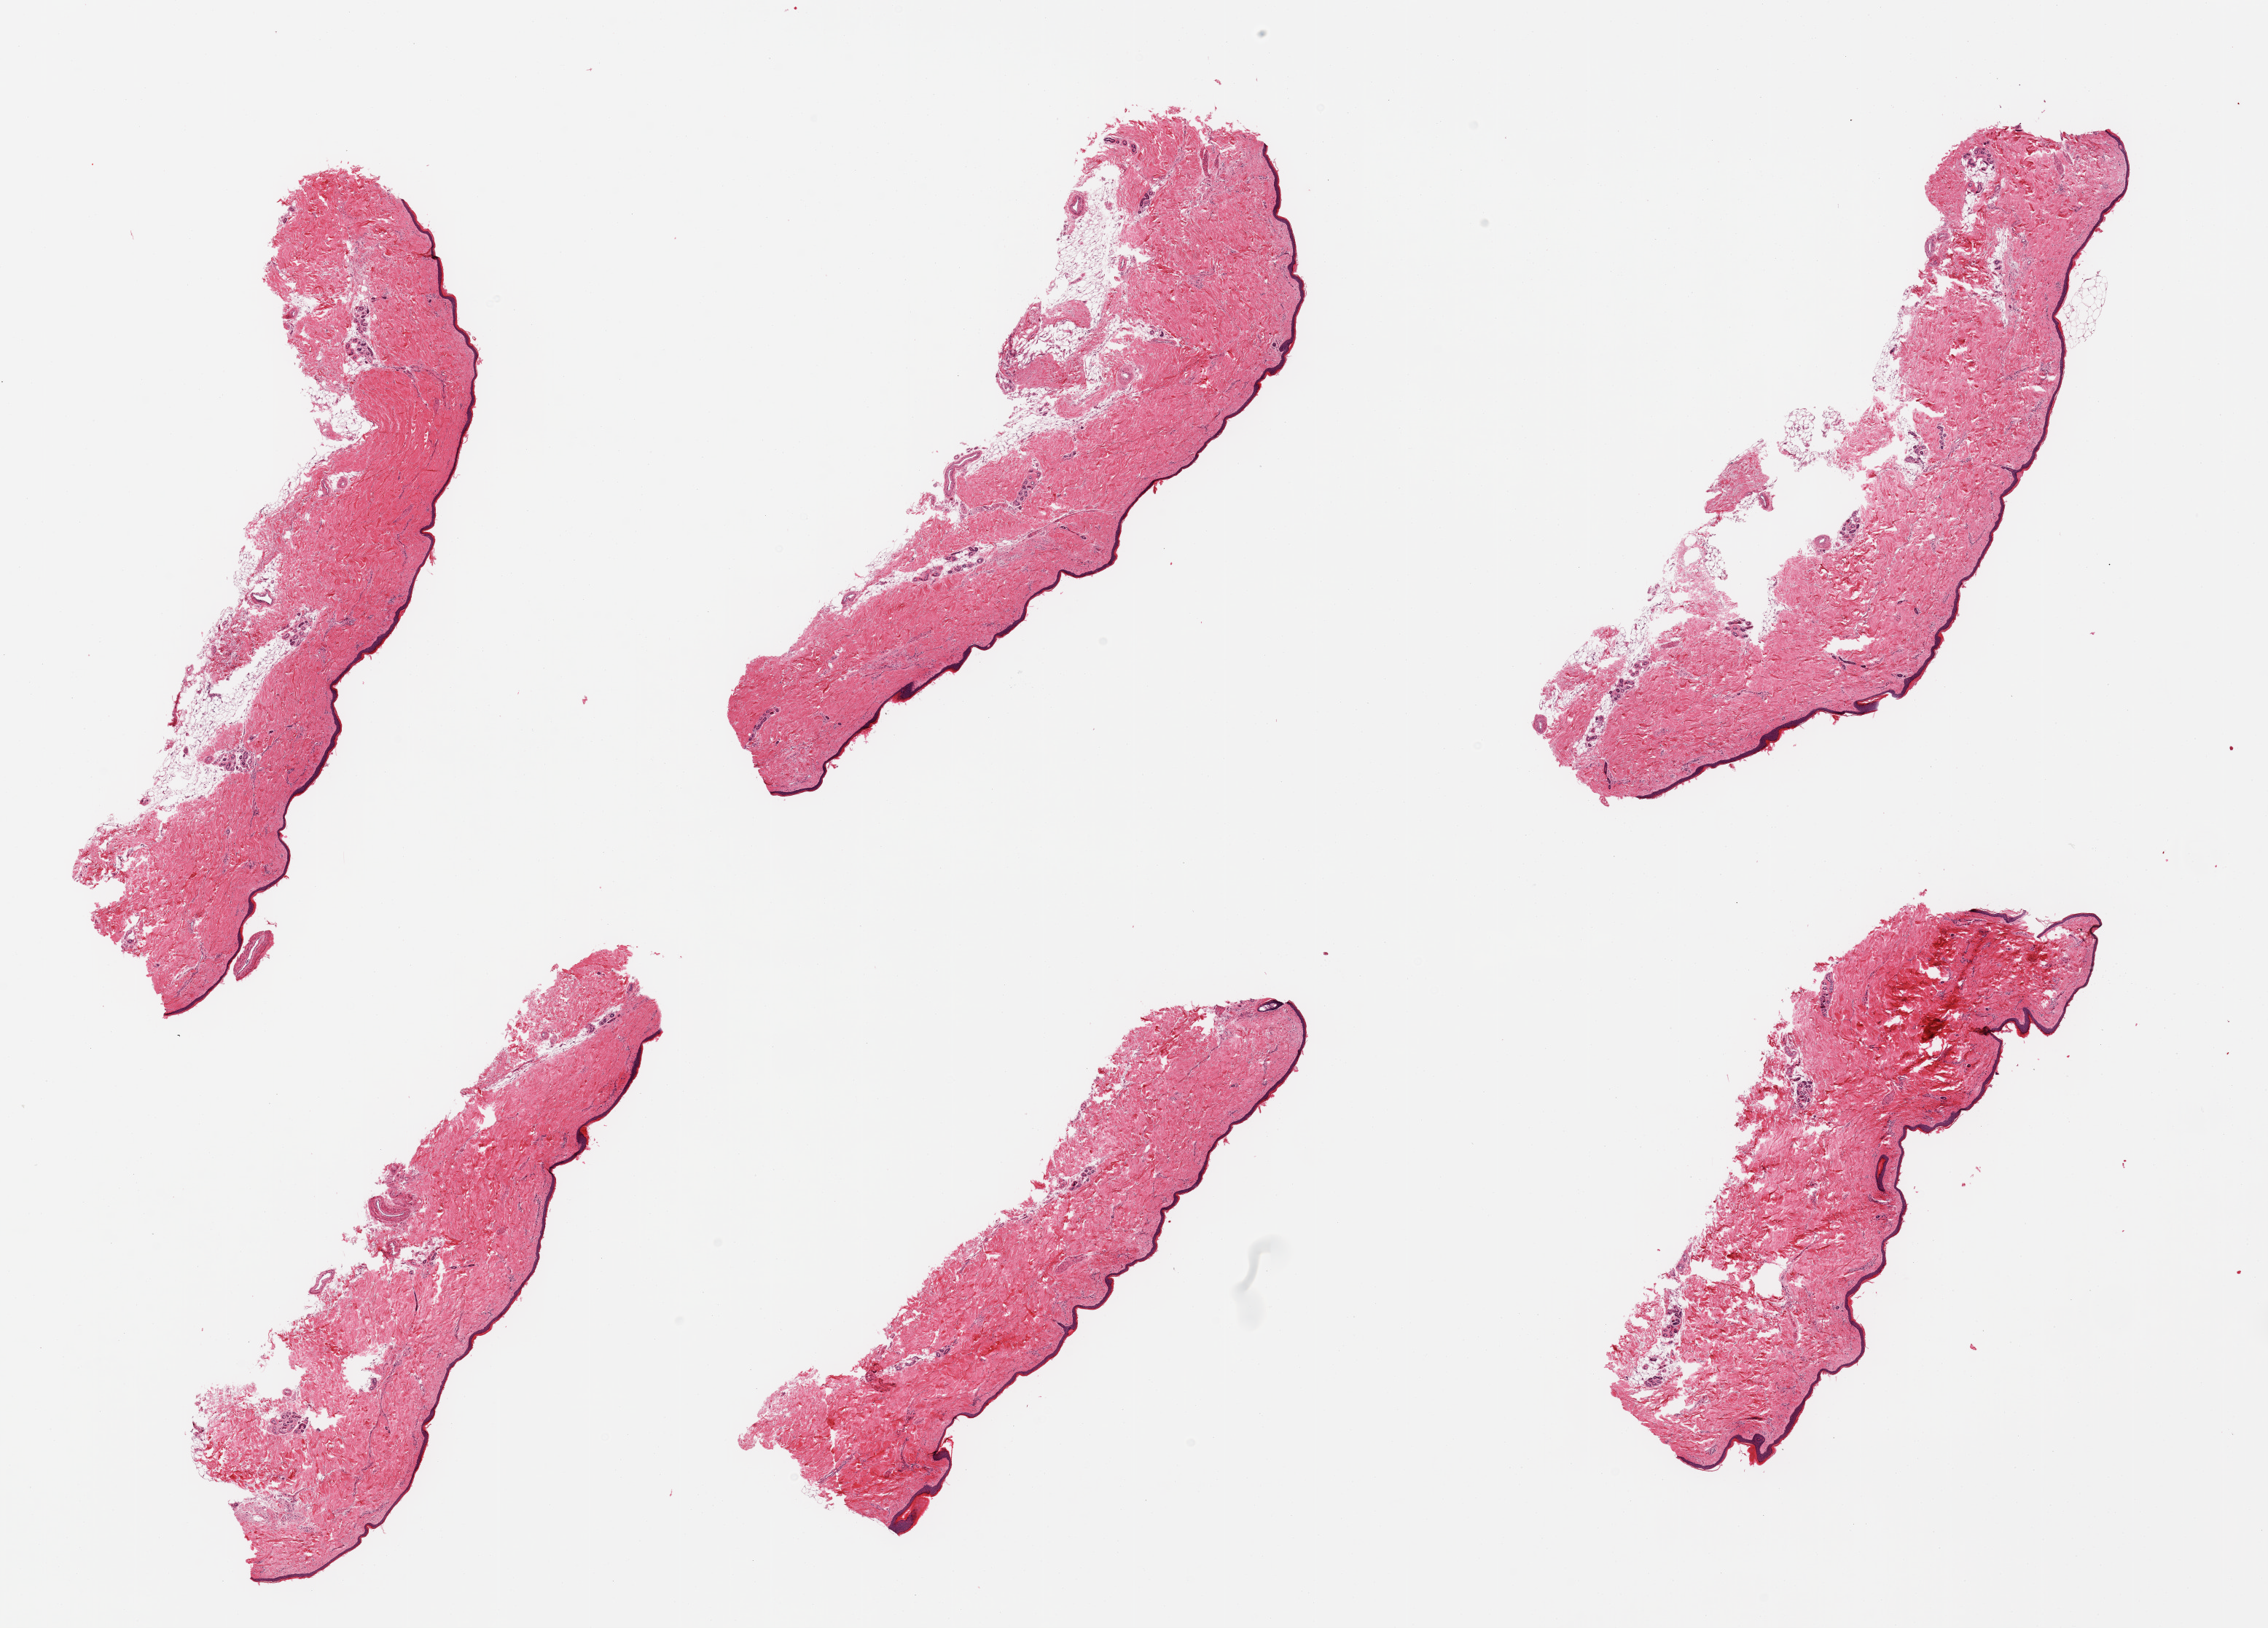
Hematoxylin and eosin (H&E) whole-slide image — whole scanned area (about 24.6 x 17.7 mm) shown as a low-resolution overview. PAXgene-fixed paraffin-embedded (PFPE) section. Section of skin of lower leg (target tissue). Tissue donor sample. Male donor.
Review note (as recorded): 6 pieces; ~10% external/internal fat; squamous epithelium 22 to 28 micron thick.